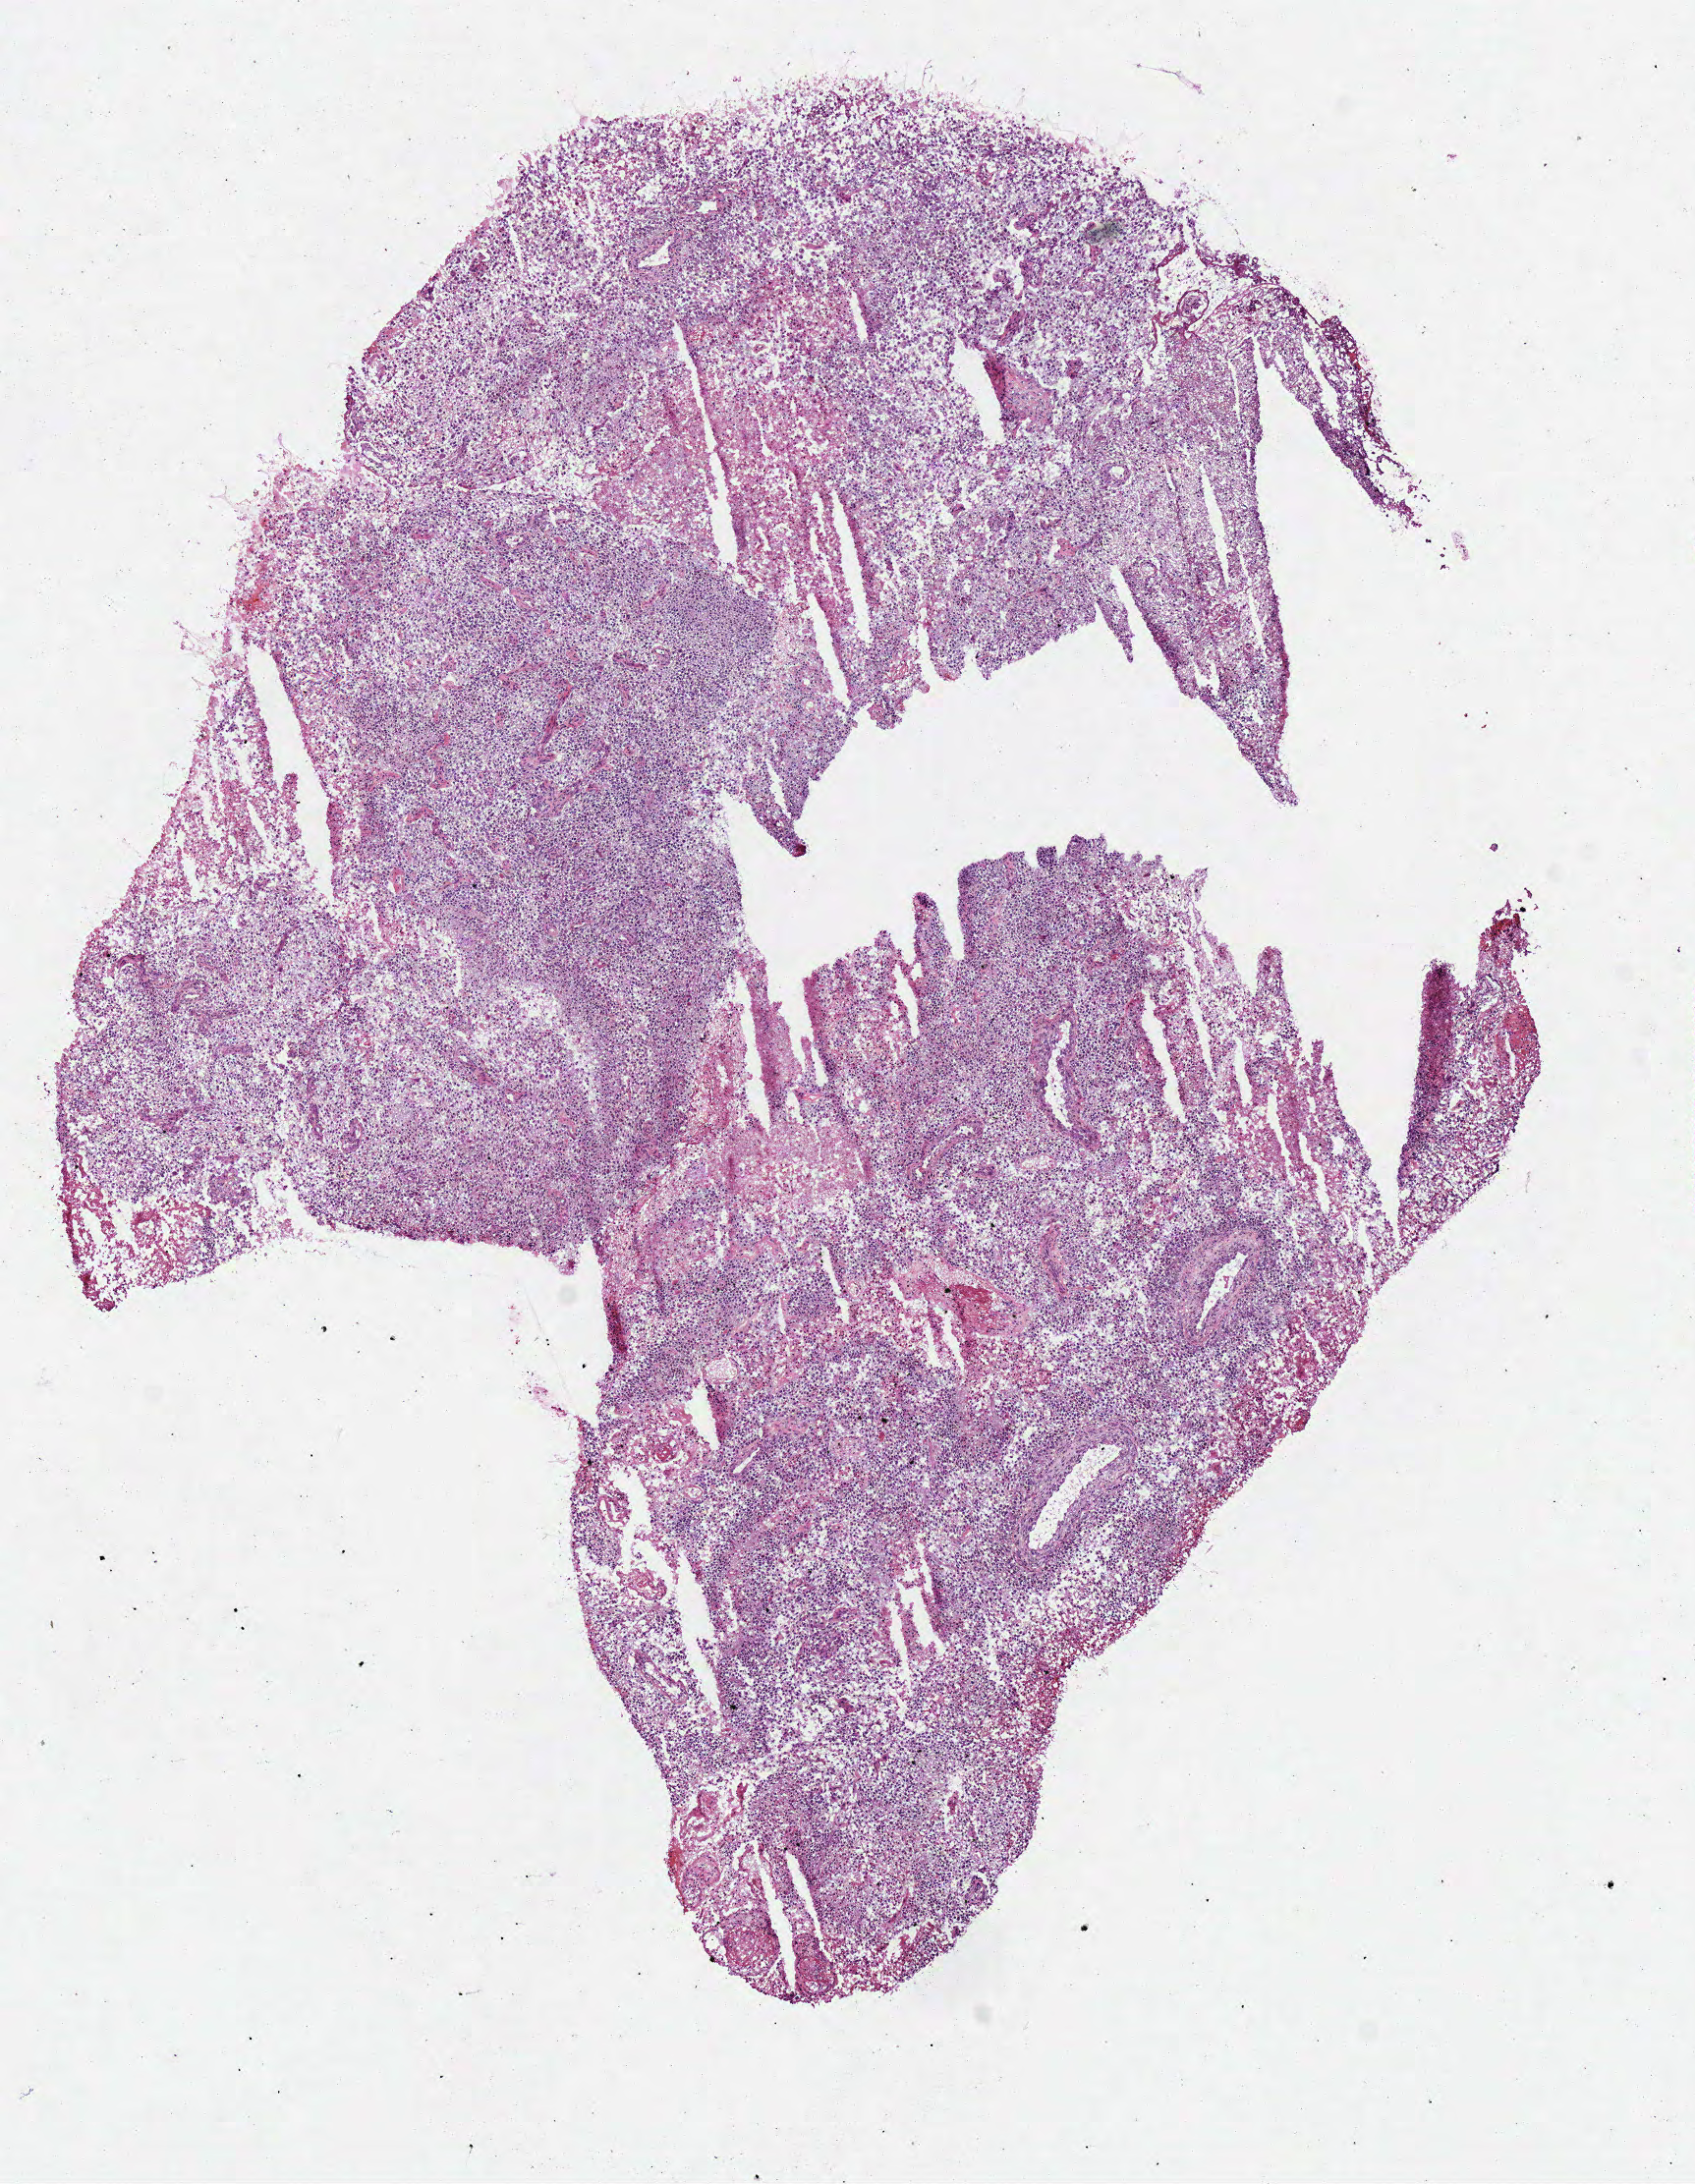
Whole-slide histology image, Hematoxylin and eosin (H&E) stained, a low-resolution overview of the entire scanned area, about 6.8 x 8.8 mm, frozen section from the bottom of the tissue portion, brain, primary tumour sample. Patient: male, age at initial diagnosis 61 years. Composition of this section per pathologist review: tumour cells 85%, tumour nuclei 85%, normal cells 0%, stromal cells 0%, necrosis 15%.
* histologic diagnosis: Glioblastoma